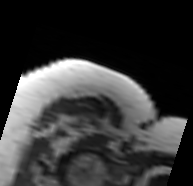
MRI of an extremity soft-tissue mass, one axial slice. Position 66 of 91 along the scan axis. MR volume resampled by the dataset authors to the PET/CT grid (not the native acquisition matrix). 3.27 mm slice thickness. 193 × 186 image matrix. Female patient. Case-level facts recorded for this patient, not image findings: histological type: malignant solitary fibrous tumor; grade: intermediate; site of the primary tumour: right thigh.
Annotated regions visible in this slice (expert contour drawn on MRI and transferred to this co-registered scan by the dataset authors):
- gross tumour volume including surrounding oedema: box from (x=51, y=112) to (x=114, y=150) px